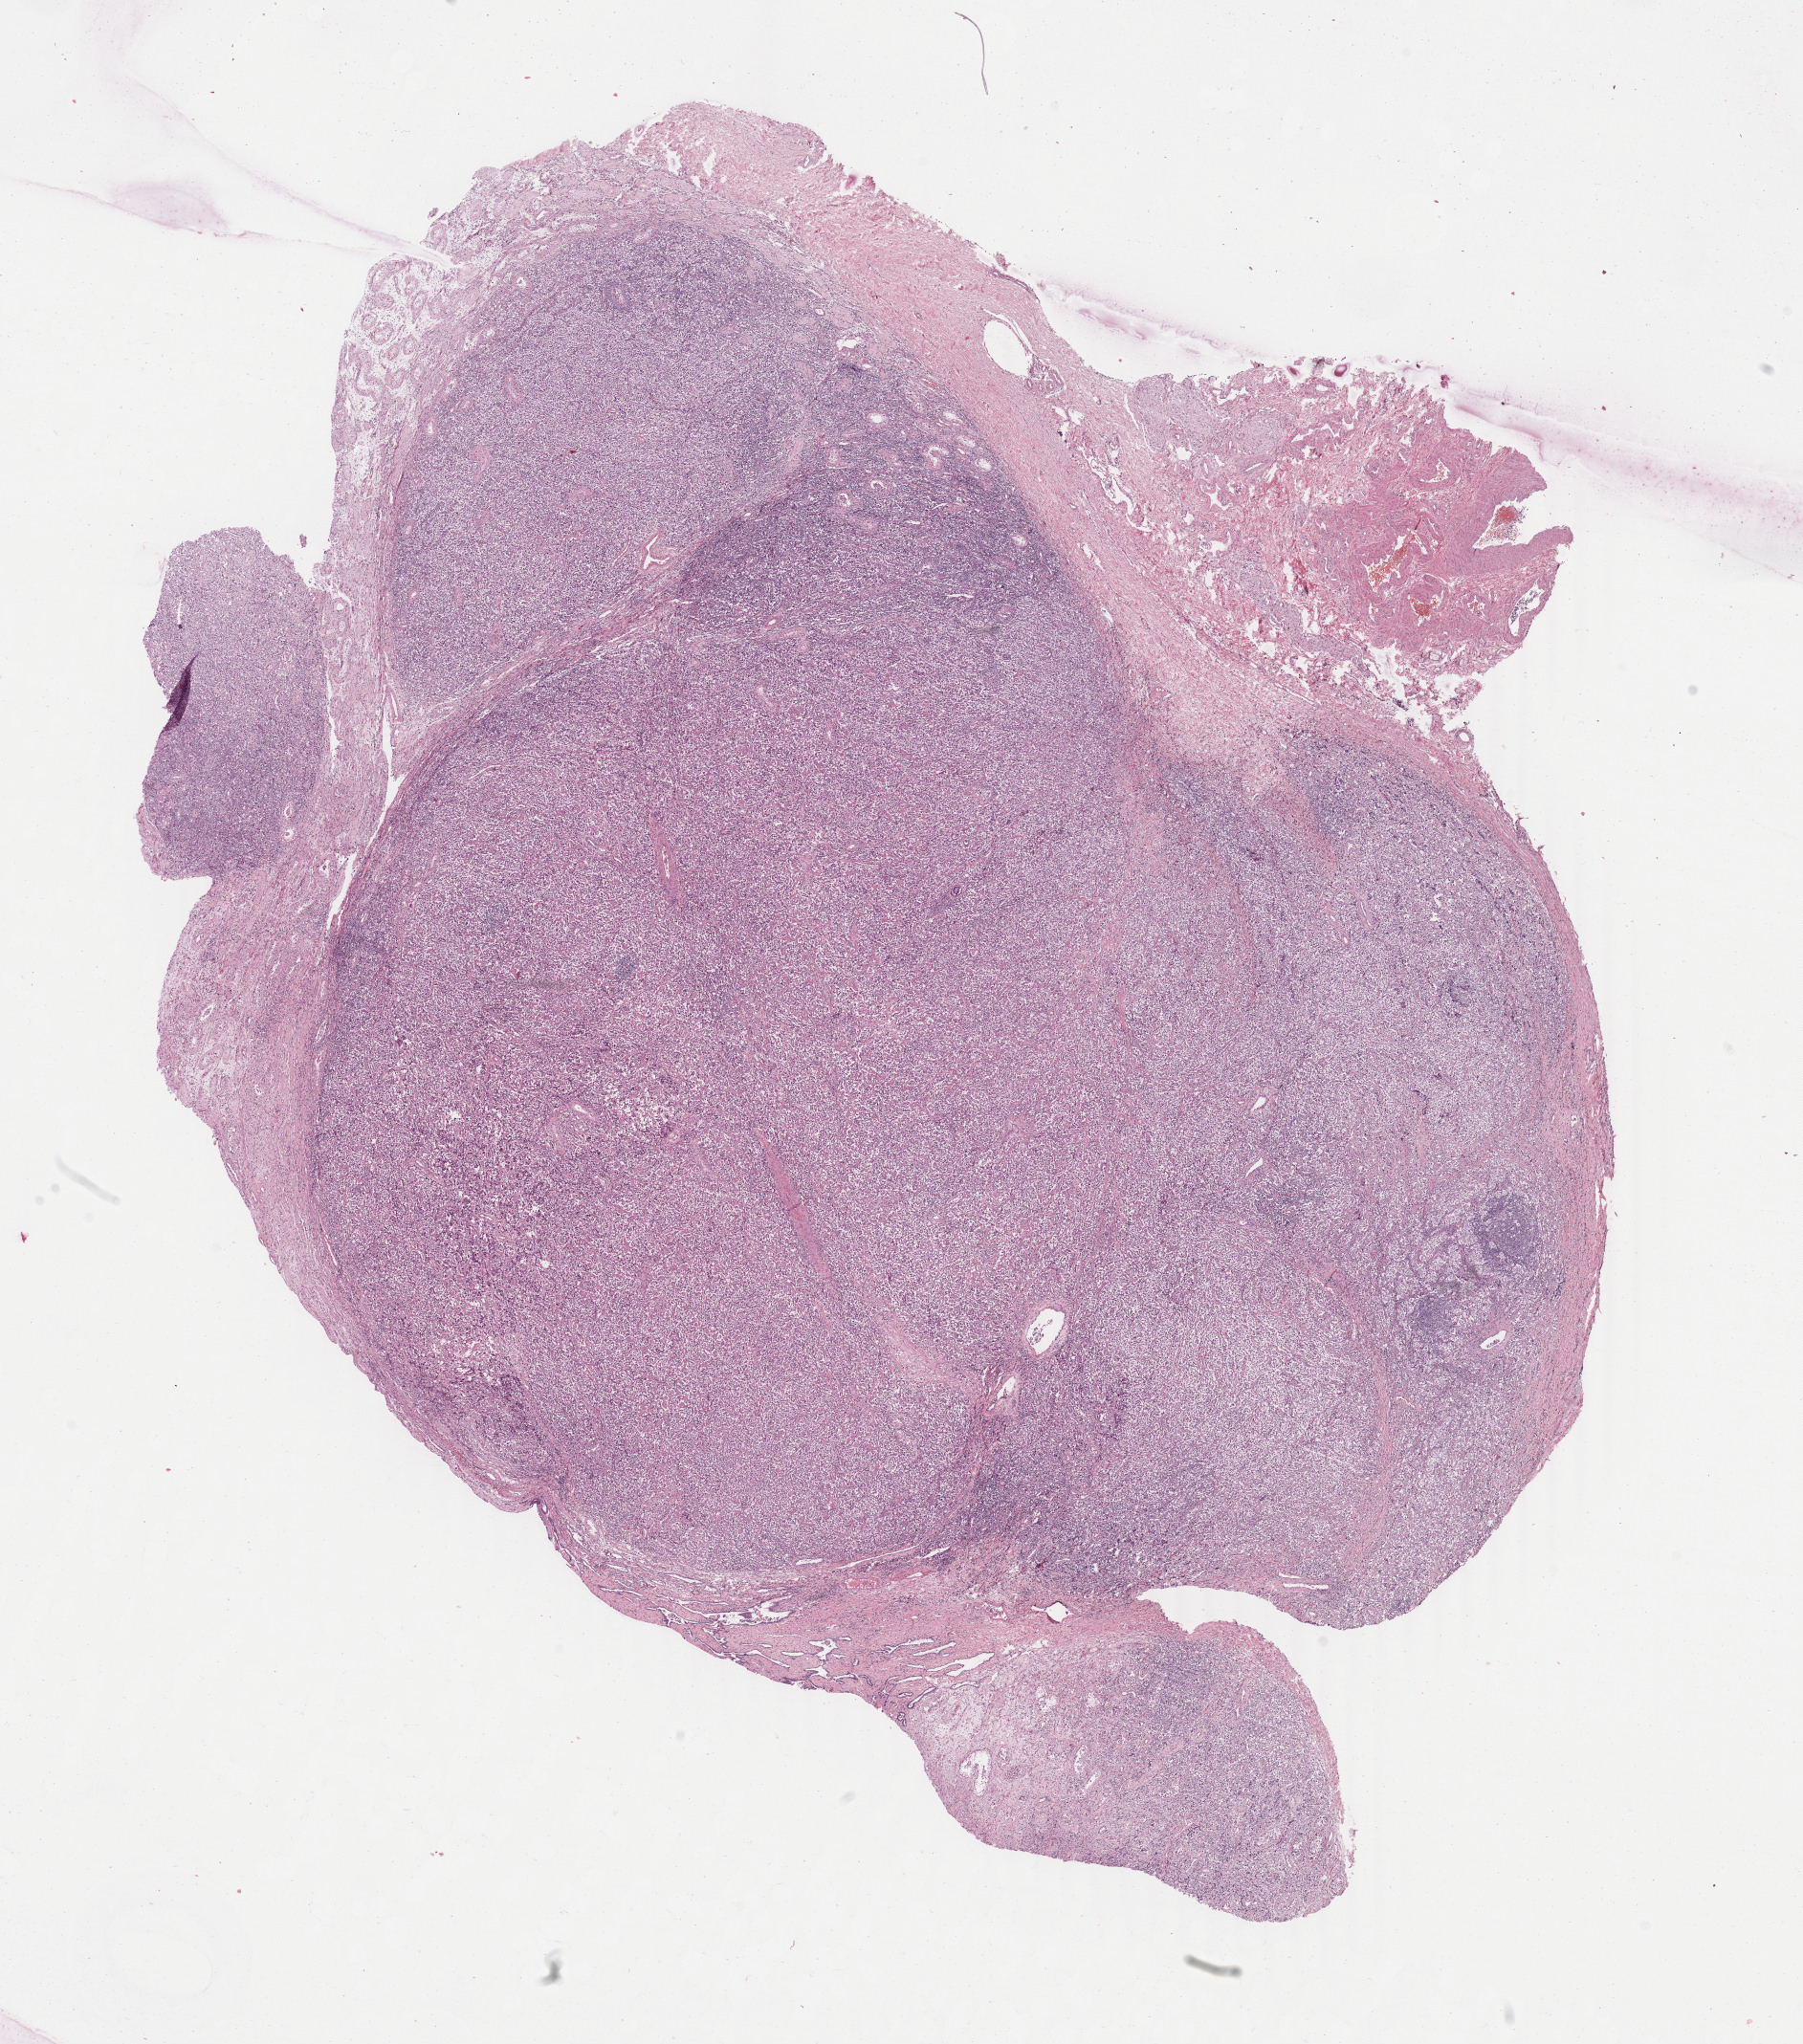
Digitized Hematoxylin and eosin (H&E) stained tissue section (whole slide), shown as a low-resolution overview of the whole scanned area (about 15.0 x 17.0 mm); formalin-fixed paraffin-embedded (FFPE) diagnostic section; testis, primary tumour sample. Male patient; age at initial diagnosis 26 years.
- histologic diagnosis: Seminoma, NOS
- TNM: T2 N0 M0
- AJCC pathologic stage: IA